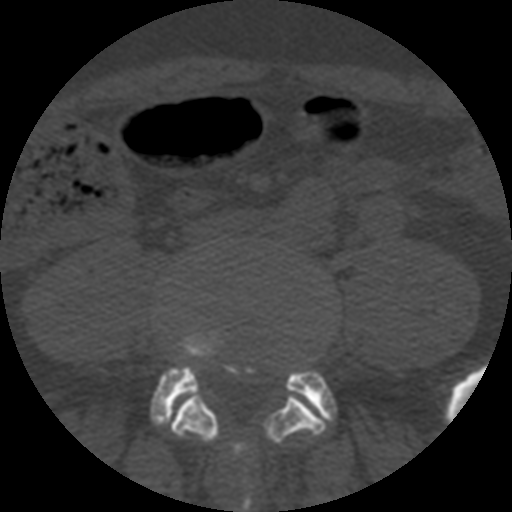
CT including the spine, one axial slice; position 77 of 508 along the scan axis; reconstruction kernel STANDARD; bone window (W 1800 / L 400 HU); 512 × 512 image matrix. Patient age 57 years. From the clinical record (not read from this slice): primary cancer: prostate.
Annotated regions visible in this slice (semi-automatically segmented with operator editing):
- L4 vertebra: bounding box <170,389,326,482> (left, top, right, bottom; pixels)
- L5 vertebra: <151,332,336,512>